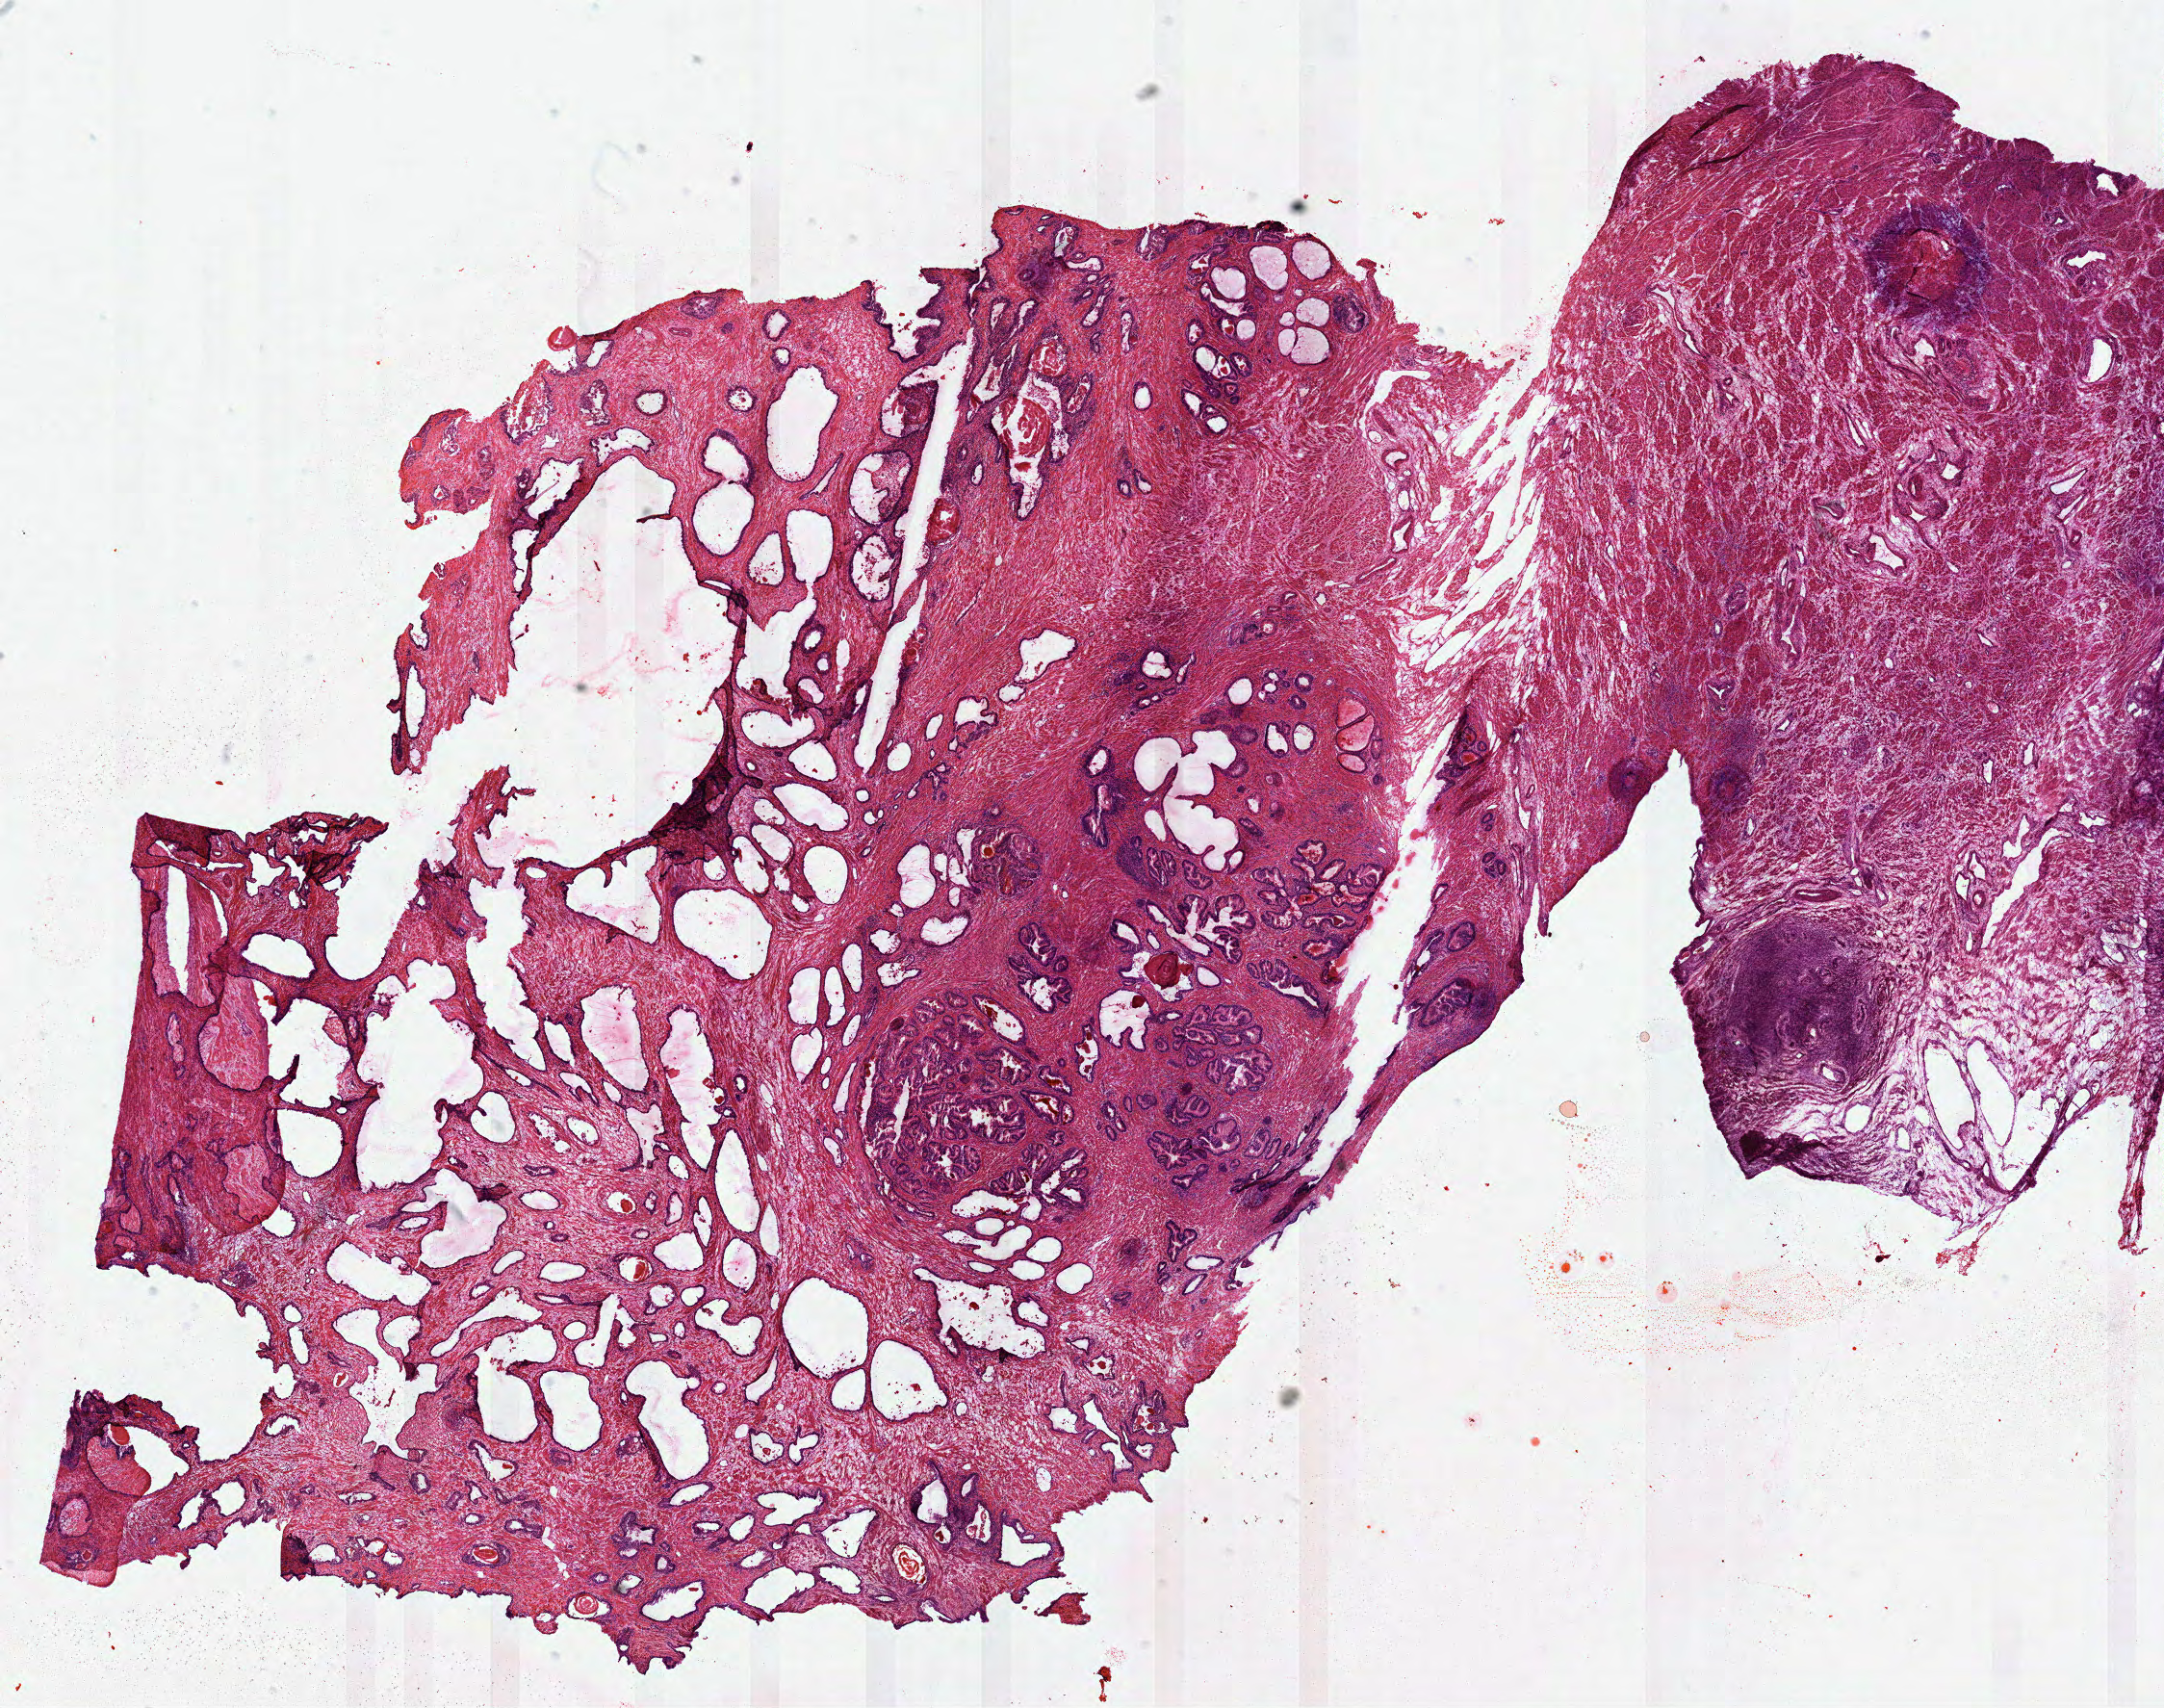
Digitized H&E-stained tissue section (whole slide) — shown as a low-resolution overview of the whole scanned area (about 18.1 x 14.3 mm, slide scanned at 40x); frozen section from the top of the tissue portion; sample: solid tissue normal (non-tumour tissue), prostate. Male patient; age at initial diagnosis 63 years.
This section: solid tissue normal sample (biorepository sample class). Patient diagnosis: Acinar cell carcinoma (prostate gland).